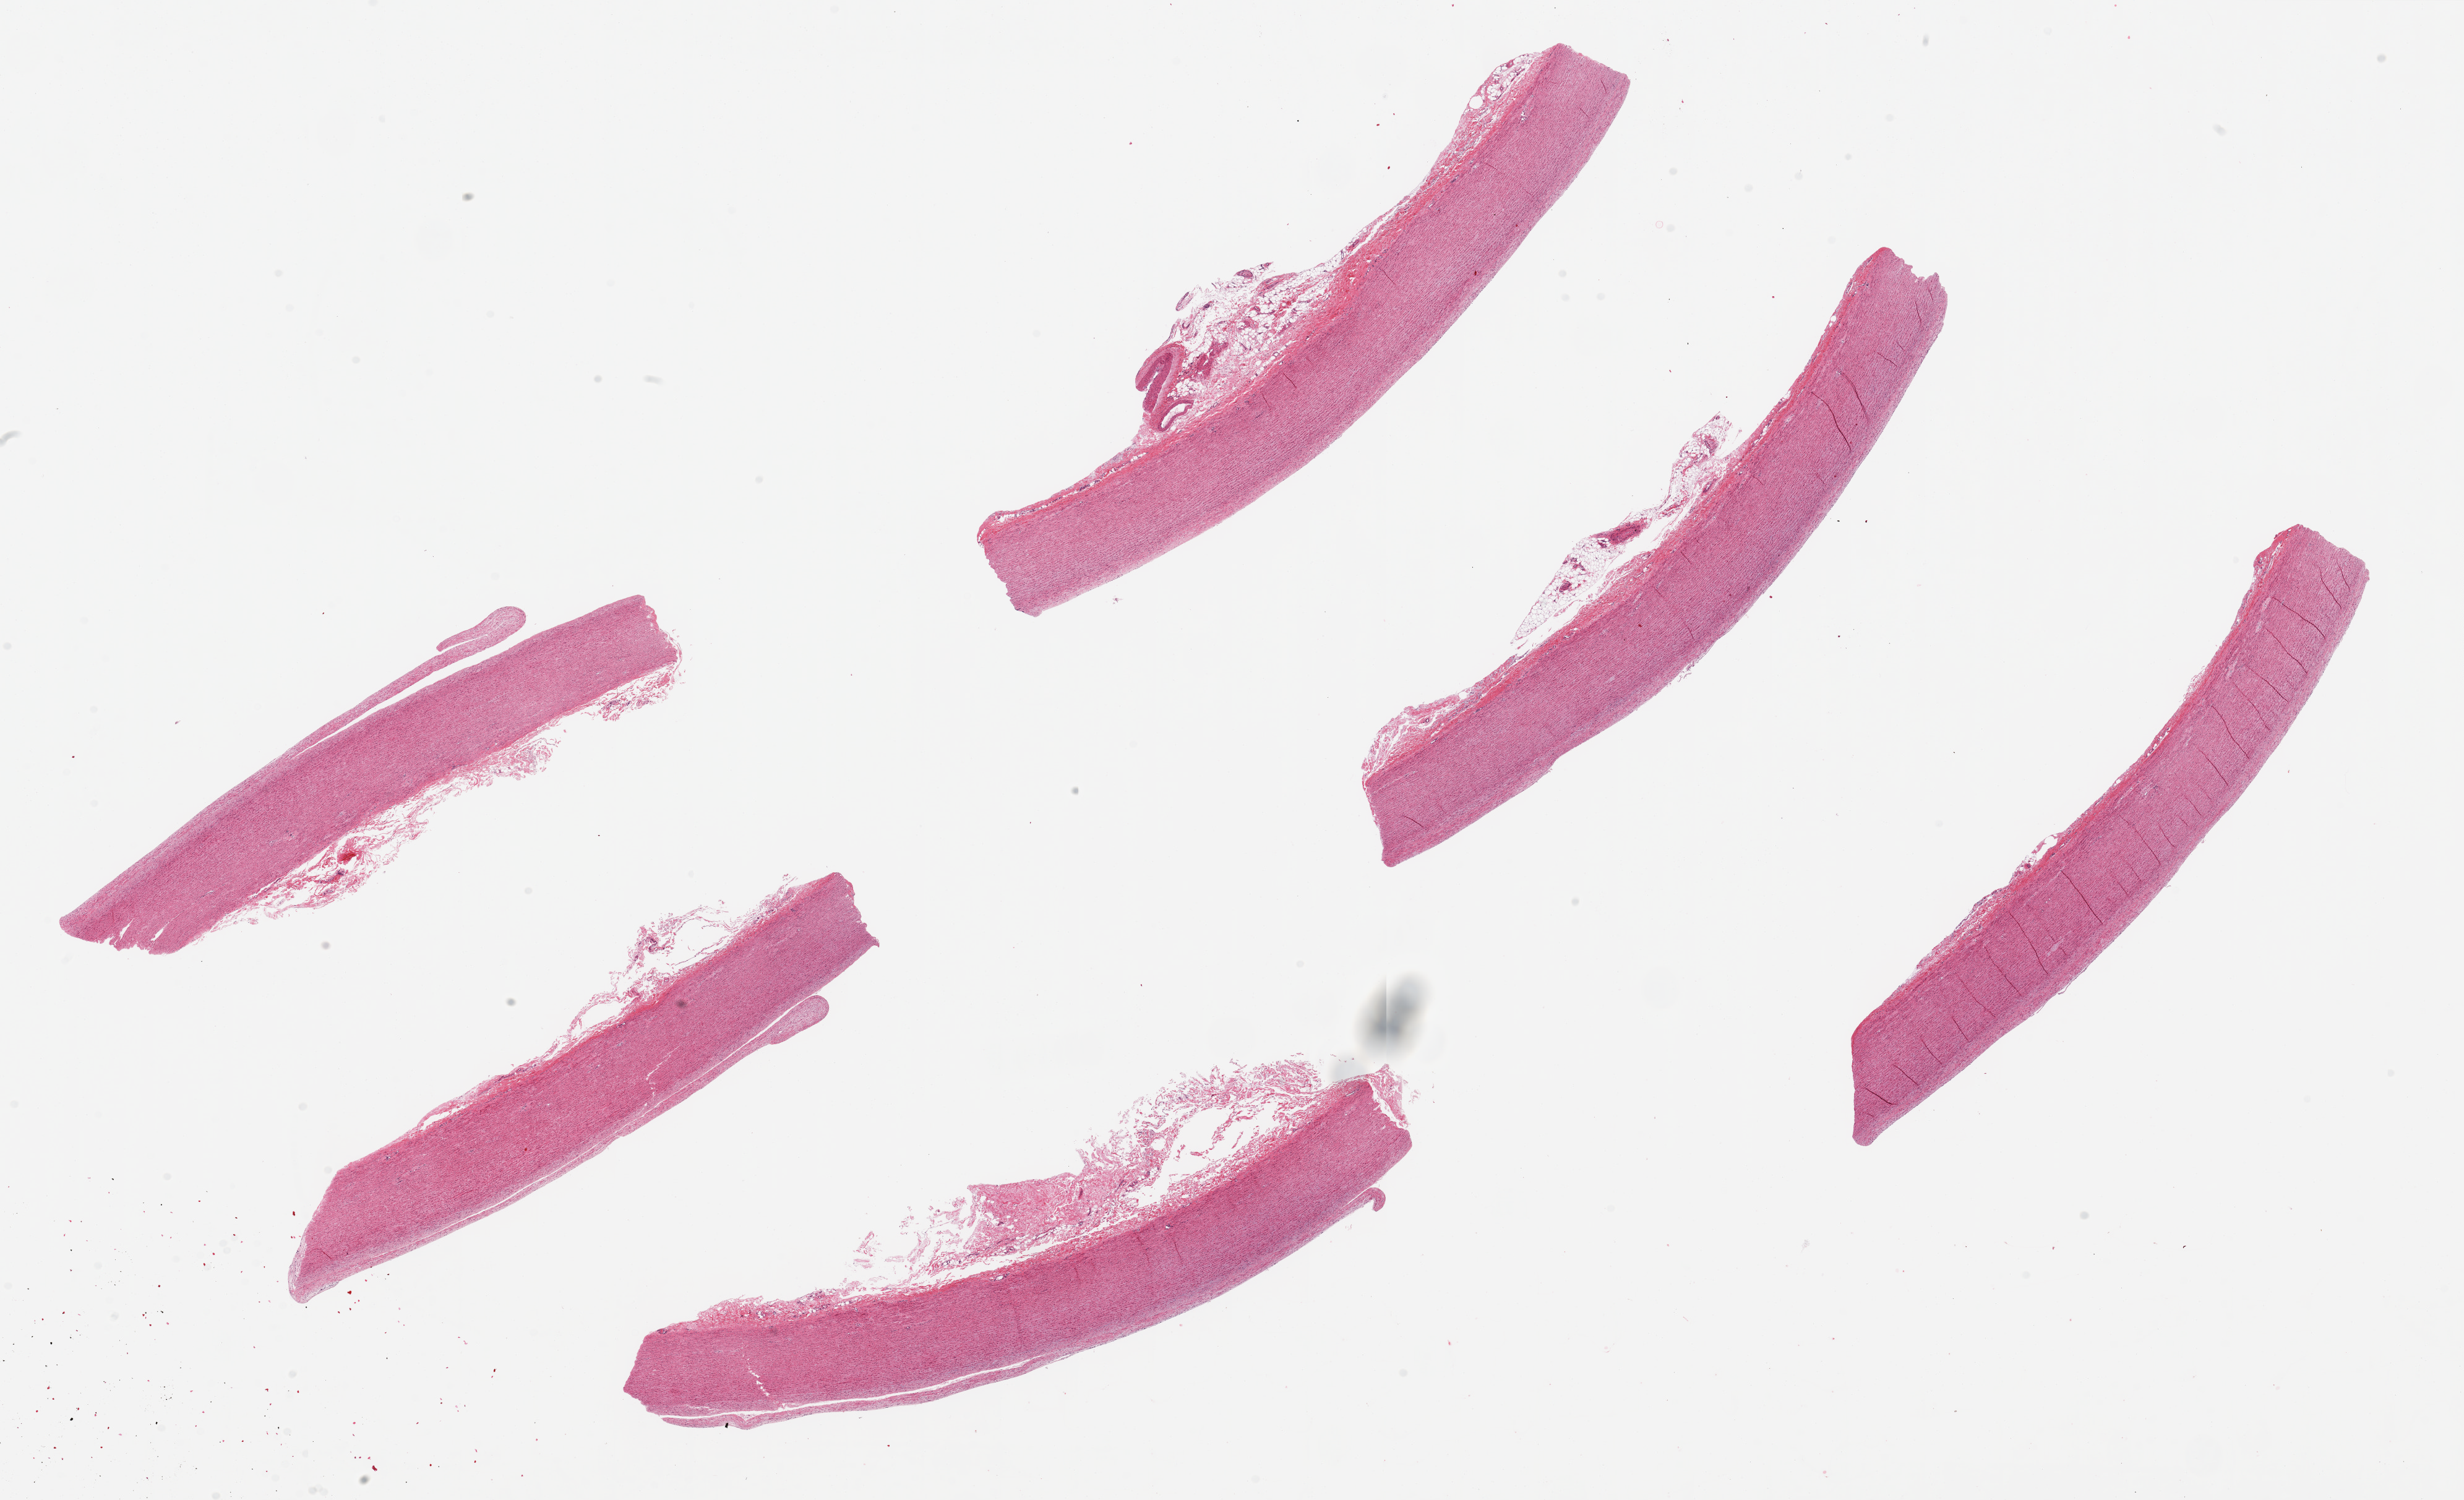
Digitized haematoxylin and eosin-stained section, shown as a low-resolution overview of the whole scanned area (about 31.5 x 19.2 mm). PAXgene-fixed, paraffin-embedded tissue. Target tissue: aorta. Donor tissue sample.
Review note (as recorded): 6 pieces. 10x1.3mm. no fatty deposits. Sparse adherent stroma.